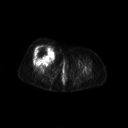
FDG PET of an extremity soft-tissue mass (from a PET/CT study), one axial slice; position 50 of 267 along the scan axis; 3.27 mm slice thickness; 128 × 128 image matrix, field of view 700 × 700 mm. Female patient, age 56 years. Case-level facts recorded for this patient, not image findings: histological type: malignant solitary fibrous tumor; grade: intermediate; site of the primary tumour: right thigh.
Annotated regions visible in this slice (expert contour drawn on MRI and transferred to this co-registered scan by the dataset authors):
- gross tumour volume including surrounding oedema: bounding box (x1, y1, x2, y2) in pixels: (31, 45, 55, 62)
- gross tumour volume (mass): (32, 45, 54, 62)